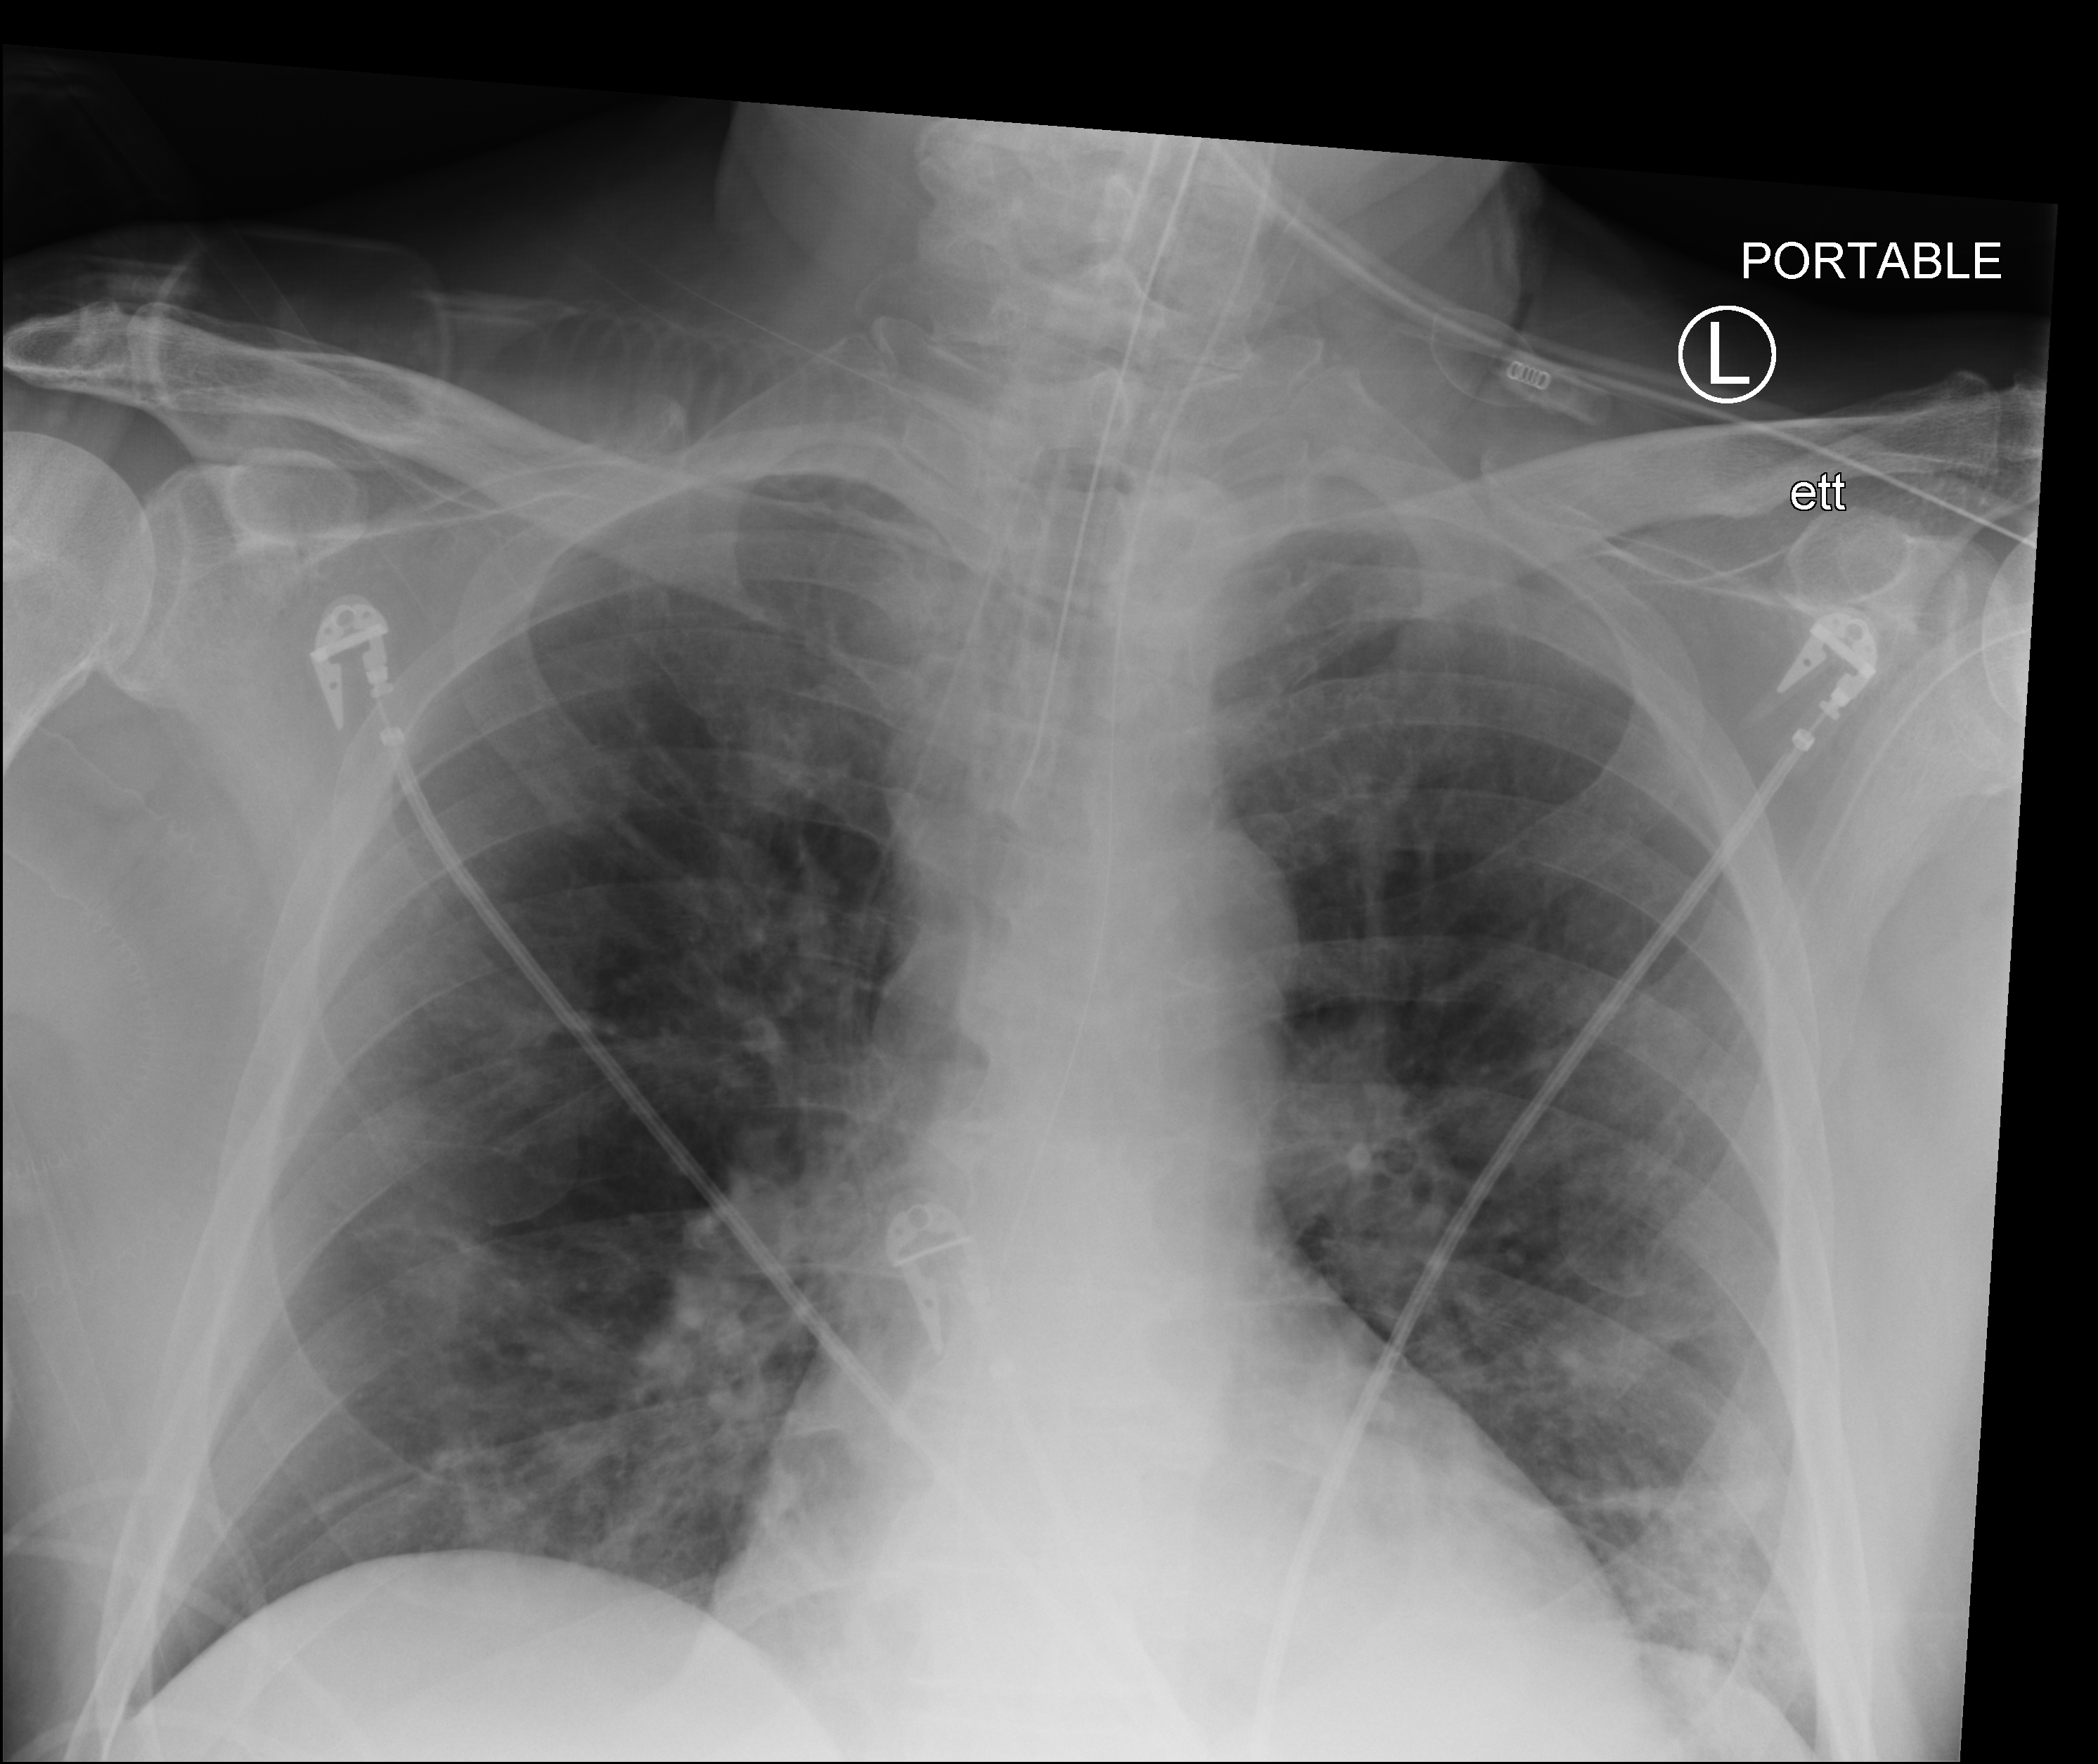
Portable chest radiograph; anteroposterior (AP) projection. Patient hospitalised with COVID-19; male, aged 60–74 years.
From the hospital-stay record, not from the radiograph (when in the stay this image was taken is not recorded):
- admitted to intensive care during this hospital stay: yes
- mechanically ventilated during this hospital stay: yes
- smoking status (admission record): never